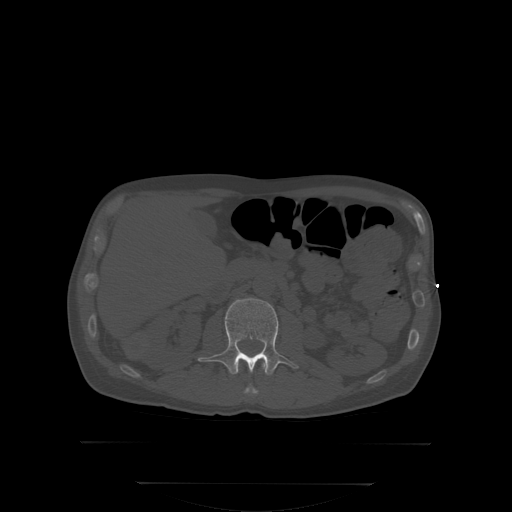
CT including the spine, one axial slice; slice 140 of 350 in the series (ordered by position); bone window (W 1800 / L 400 HU); 2.5 mm slice thickness; 512 × 512 image matrix. Patient: male, 58 years. From the clinical record (not read from this slice): primary cancer: prostate; vertebrae with lytic lesions (as recorded): L1.
Outlined on this slice (semi-automatically segmented with operator editing):
- L1 vertebra: bounding box <246,364,265,396> (left, top, right, bottom; pixels)
- L2 vertebra: <198,297,299,388>